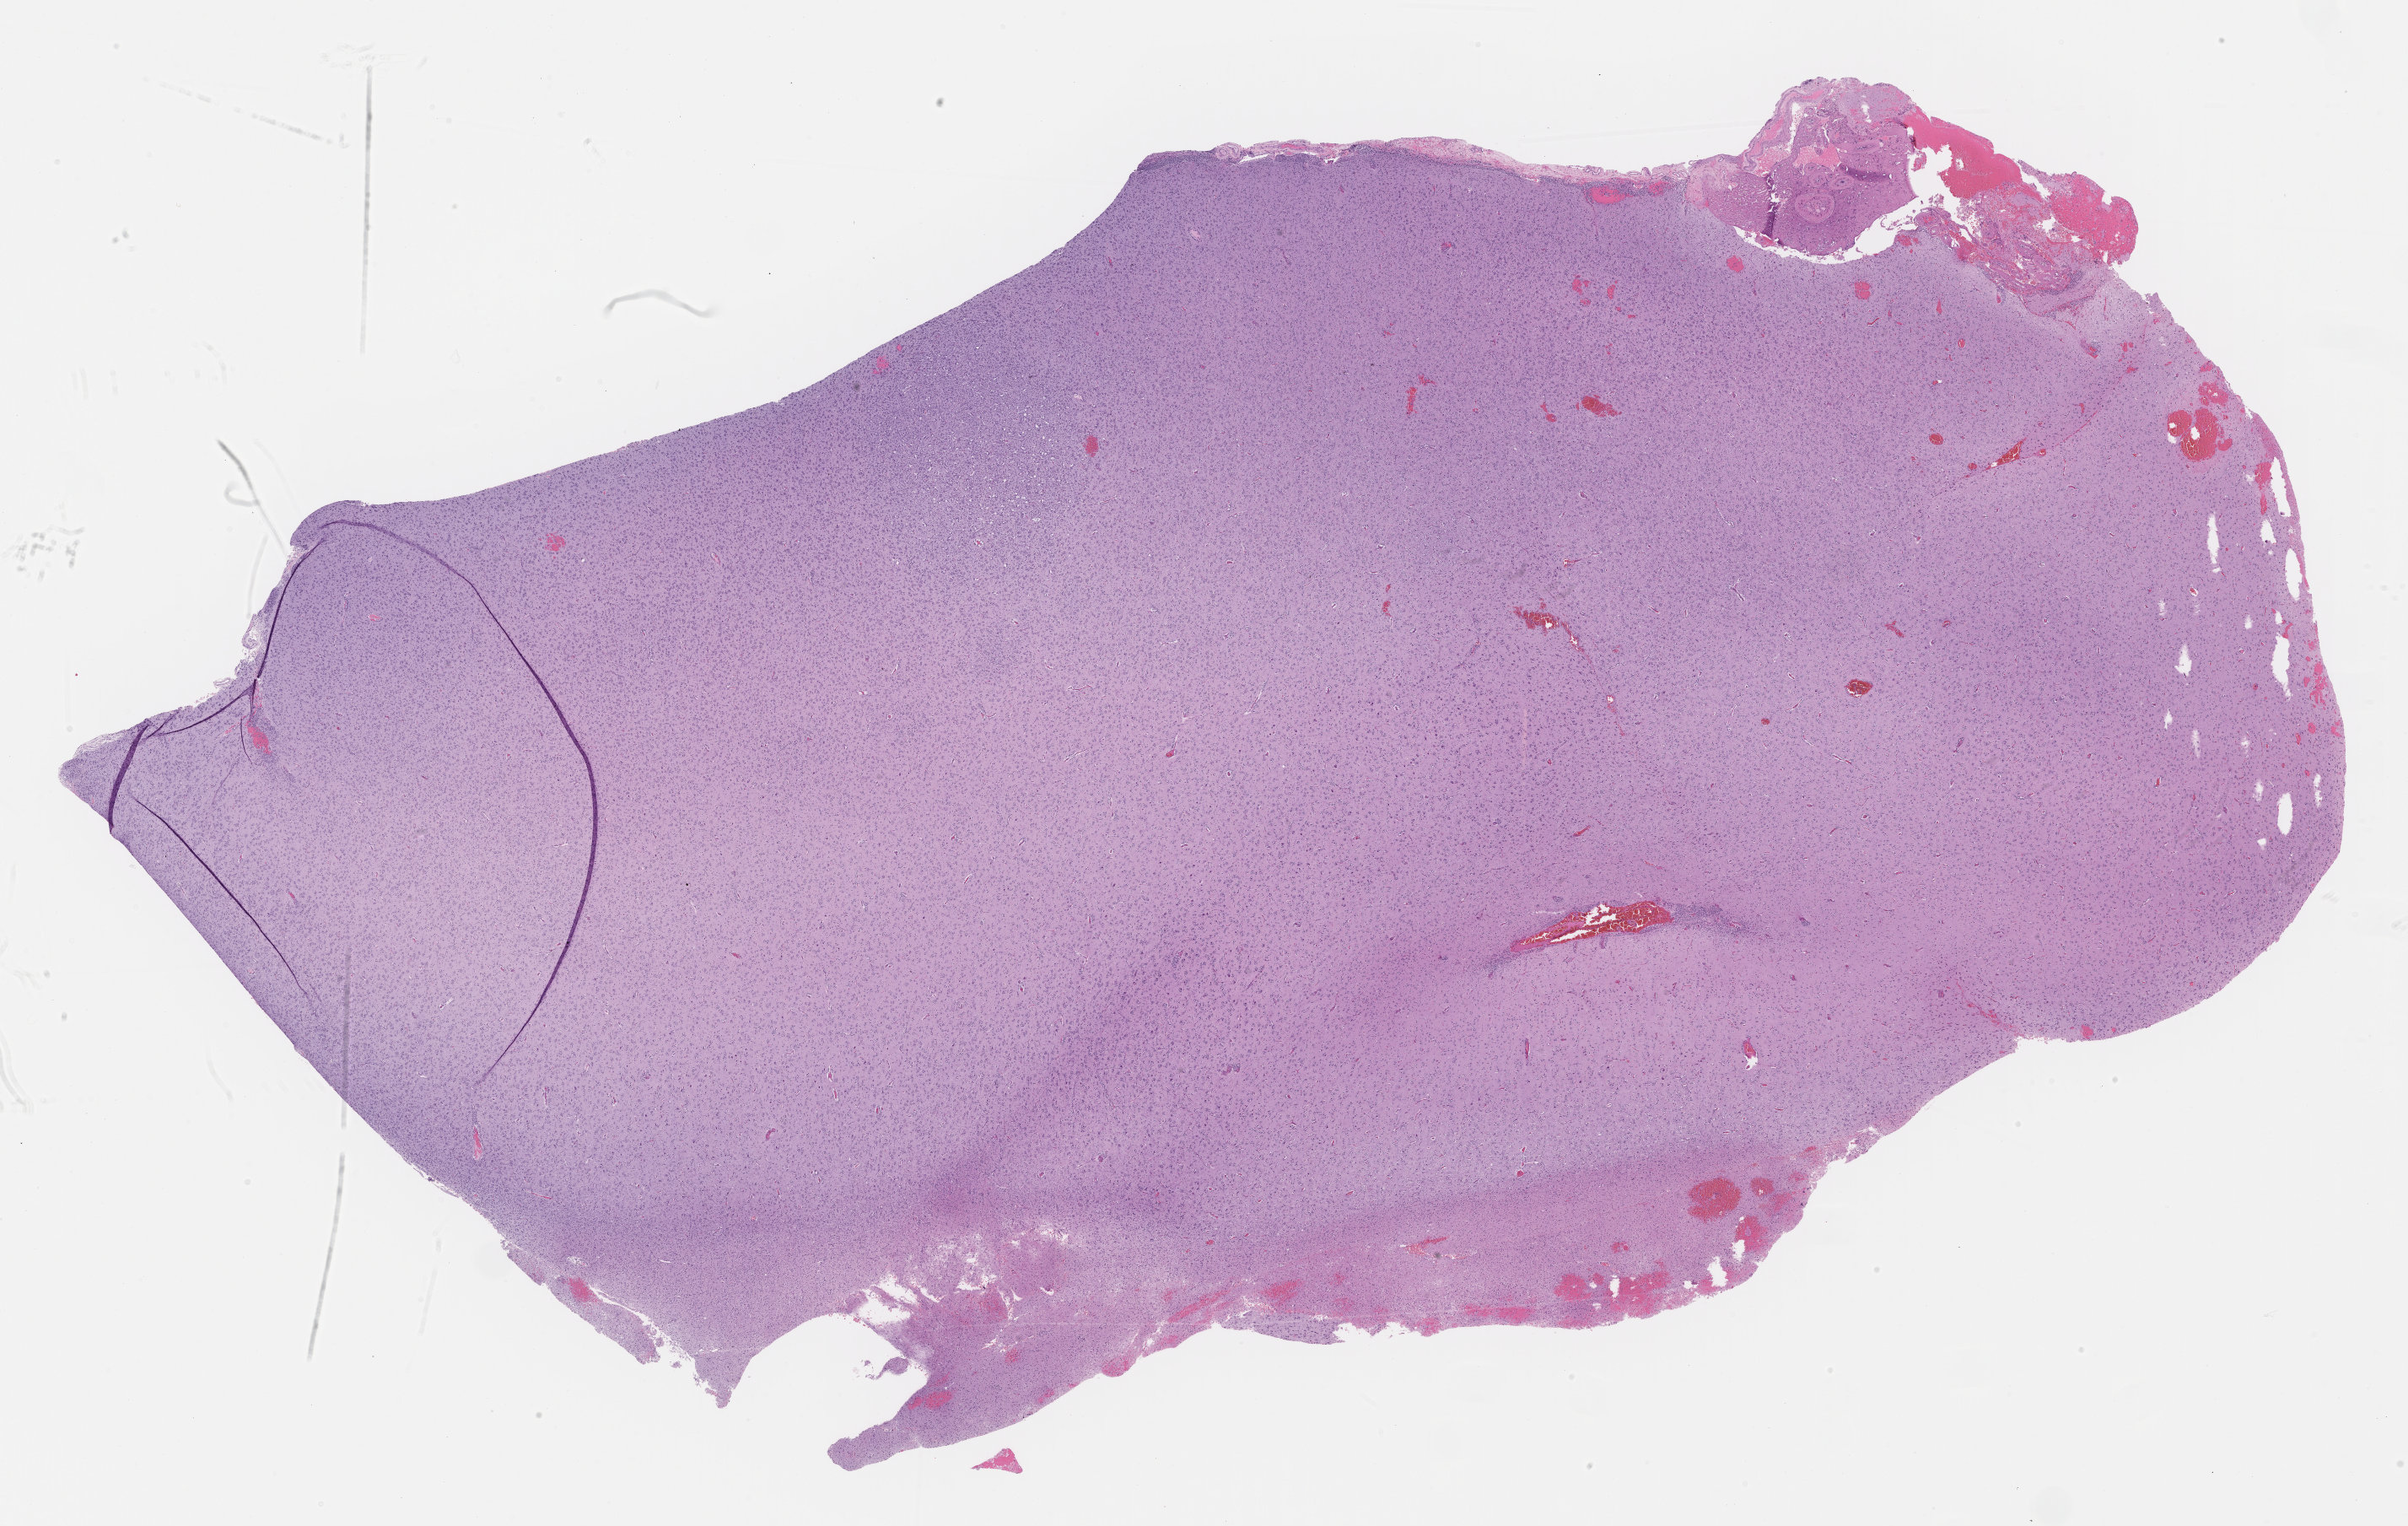
Digitized Hematoxylin and eosin (H&E) stained tissue section (whole slide), whole scanned area (about 23.0 x 14.6 mm, slide scanned at 40x) shown as a low-resolution overview. Formalin-fixed paraffin-embedded (FFPE) diagnostic section. Brain, primary tumour sample. Female, age 53 years at initial diagnosis. Histologic grade: G2 (moderately differentiated).
Laterality: right. Pathologic diagnosis: Oligodendroglioma, NOS (cerebrum).